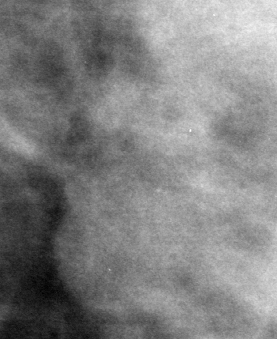
Crop from a digitized film mammogram around one marked abnormality, left breast, MLO view, BI-RADS breast density category 3 (scale 1–4).
- Finding: mass, shape round, margins microlobulated; BI-RADS assessment category 3; benign; no additional work-up was recommended (benign without callback).